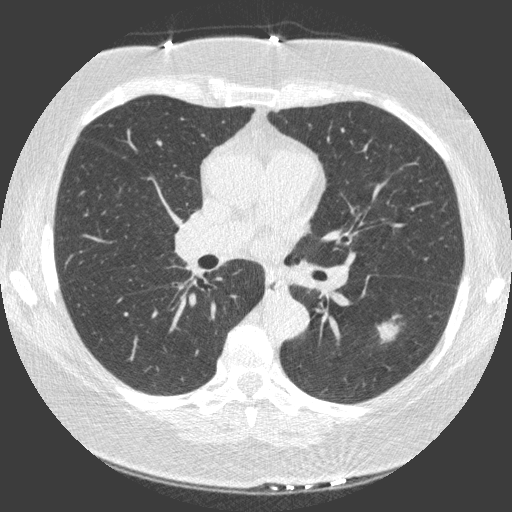
Axial slice from a low-dose chest CT screening exam, third screening round (two years after baseline), lung window (W 1500 / L -600 HU), standard (soft-tissue) reconstruction kernel (C), slice 60 of 149 in the series. Female, age 66 years at enrolment. Current smoker at enrolment.
Expert-annotated lung lesion, box from (x=366, y=302) to (x=421, y=351) px. Screening reader's record for this exam (one nodule recorded; not confirmed to be the boxed lesion): non-calcified nodule or mass ≥4 mm, left lower lobe, 23 × 17 mm, spiculated (stellate) margins, soft tissue attenuation, pre-existing on the prior screen: yes; interval growth: yes. Lung cancer was diagnosed 15 days after this screen: non-small cell carcinoma, left lower lobe, poorly differentiated (G3), stage IA (AJCC 6th edition), 20 mm at pathology.